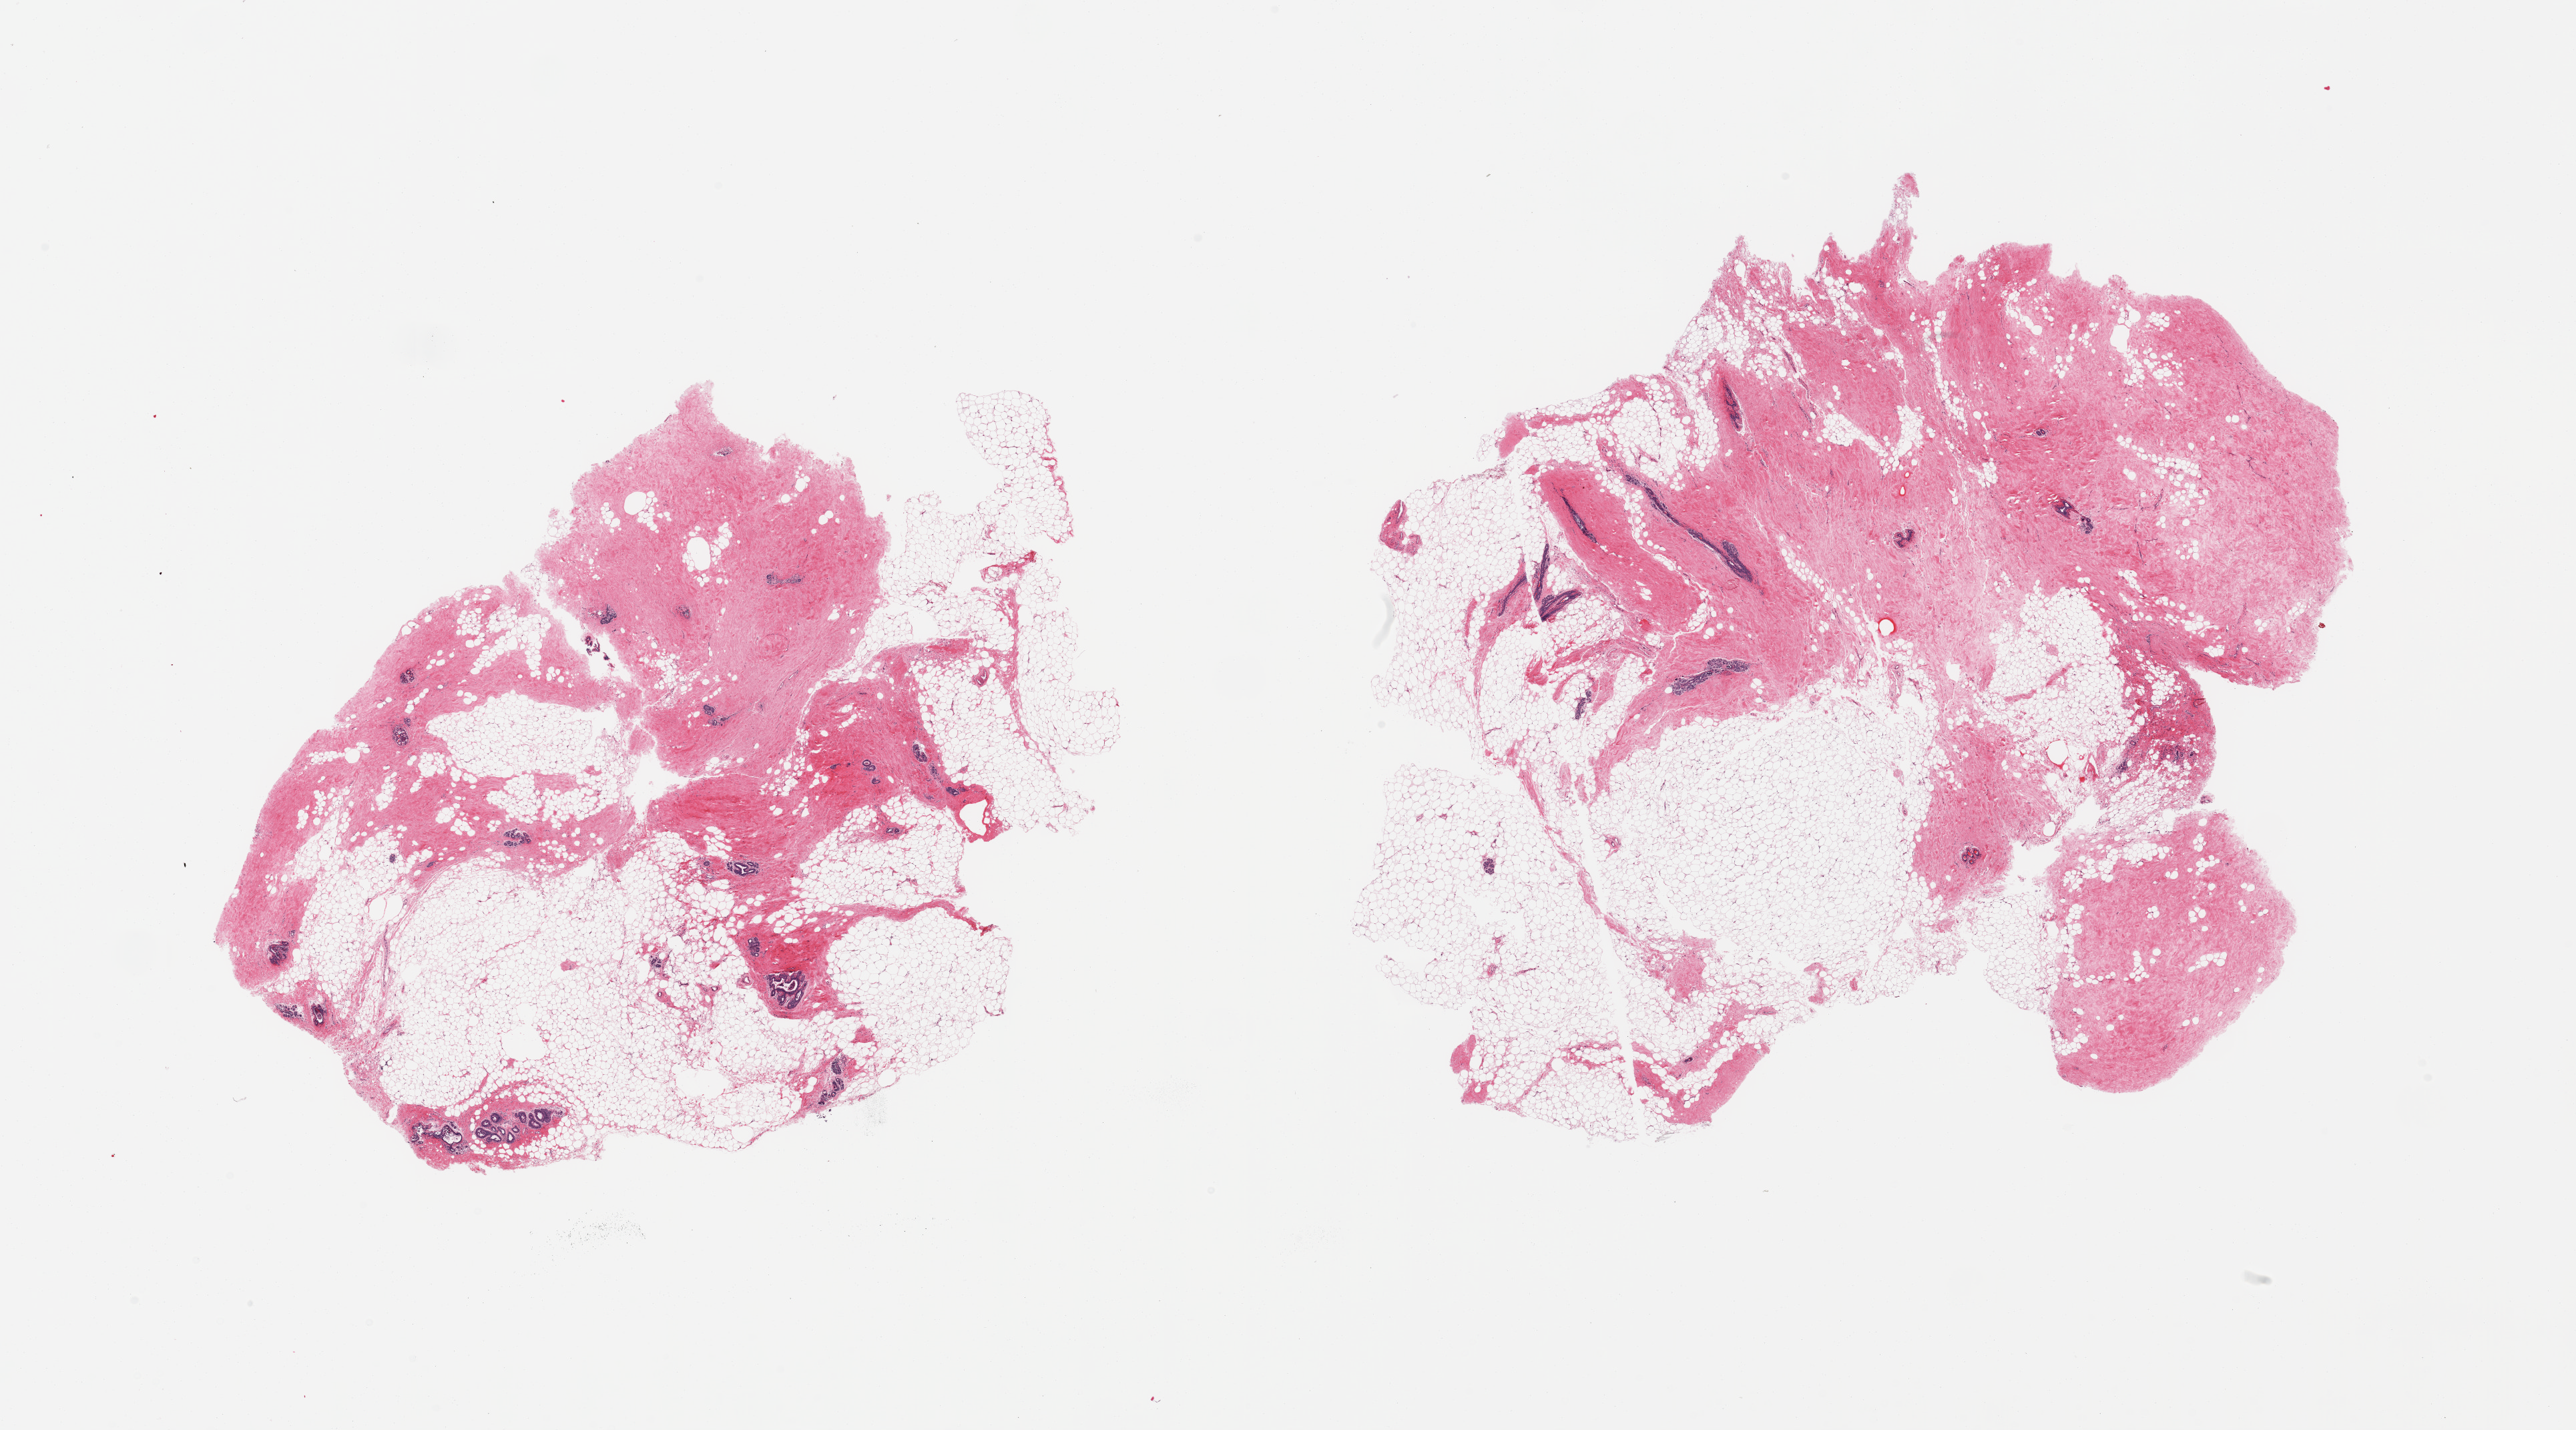
Whole-slide image, hematoxylin and eosin (H&E) stain, whole scanned area (about 30.5 x 16.9 mm) shown as a low-resolution overview; PAXgene-fixed, paraffin-embedded tissue; target tissue: breast; tissue donor sample. Donor sex: female.
Reviewer comment on this tissue sample: 2 pieces; ductal-lobular units present.